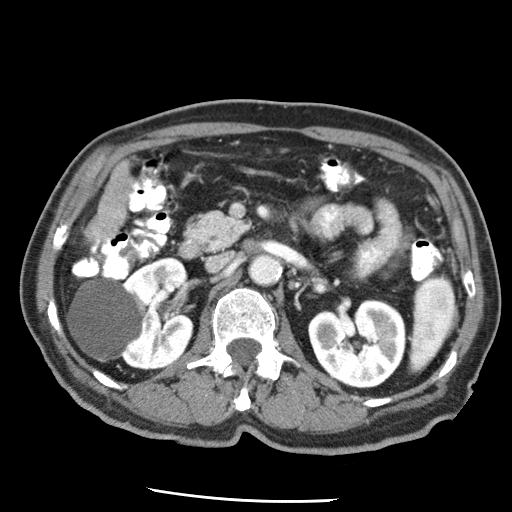
Contrast-enhanced abdominal CT (liver protocol), one axial slice; slice 10 of 79 in the series (ordered by position); soft-tissue window (W 400 / L 40 HU); 2.5 mm slice thickness; 512 × 512 image matrix, field of view 320 × 320 mm. Case-level facts recorded for this patient, not image findings: diagnosis: hepatocellular carcinoma (patient treated with transarterial chemoembolisation; whether this scan precedes or follows treatment is not stated here); TNM stage (as recorded): Stage-IIIA; Child-Pugh class: A.
Structures marked on this image (semi-automatic segmentation, software-assisted and operator-edited):
- liver parenchyma outside the tumour (the mass and vessels are separate outlines, so this box may not span the whole liver): bounding box <90,162,131,242> (left, top, right, bottom; pixels)
- liver vessels: <97,237,99,241>